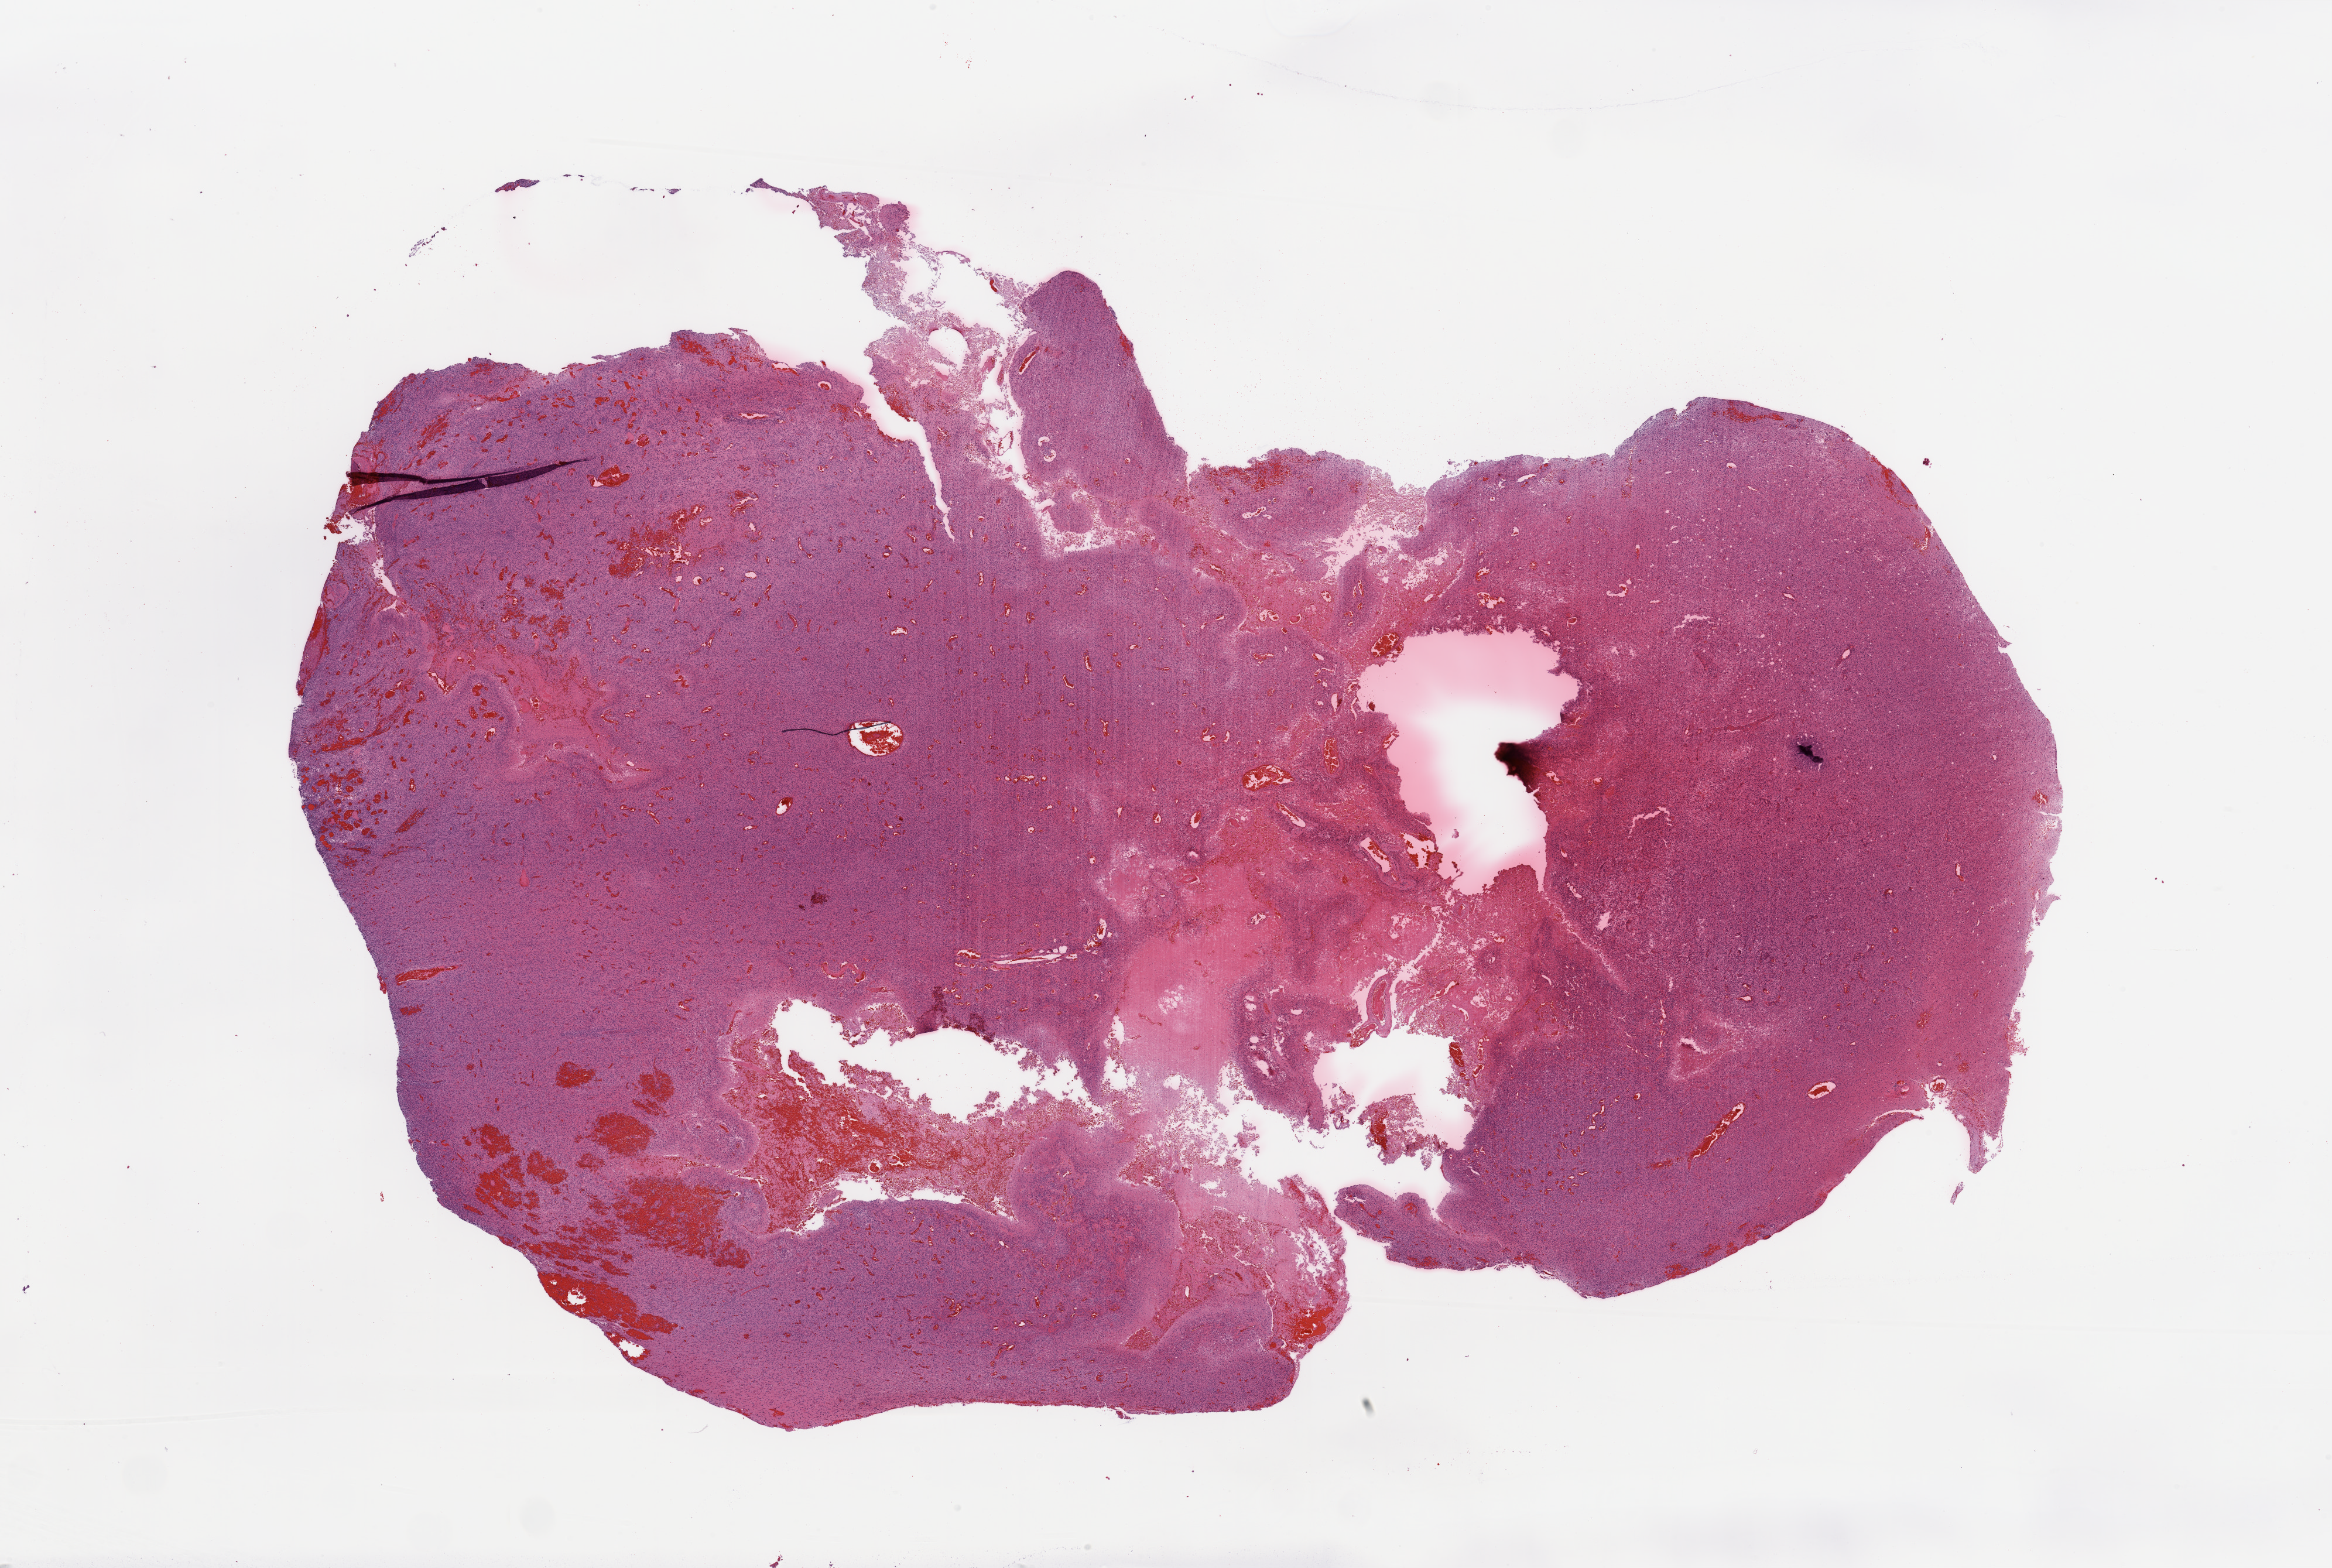
H&E-stained whole-slide image, shown as a low-resolution overview of the whole scanned area (about 31.5 x 21.2 mm), brain, tumour tissue. Female, 64 y/o.
• primary tumour site (as recorded): frontal lobe
• diagnosis: Glioblastoma